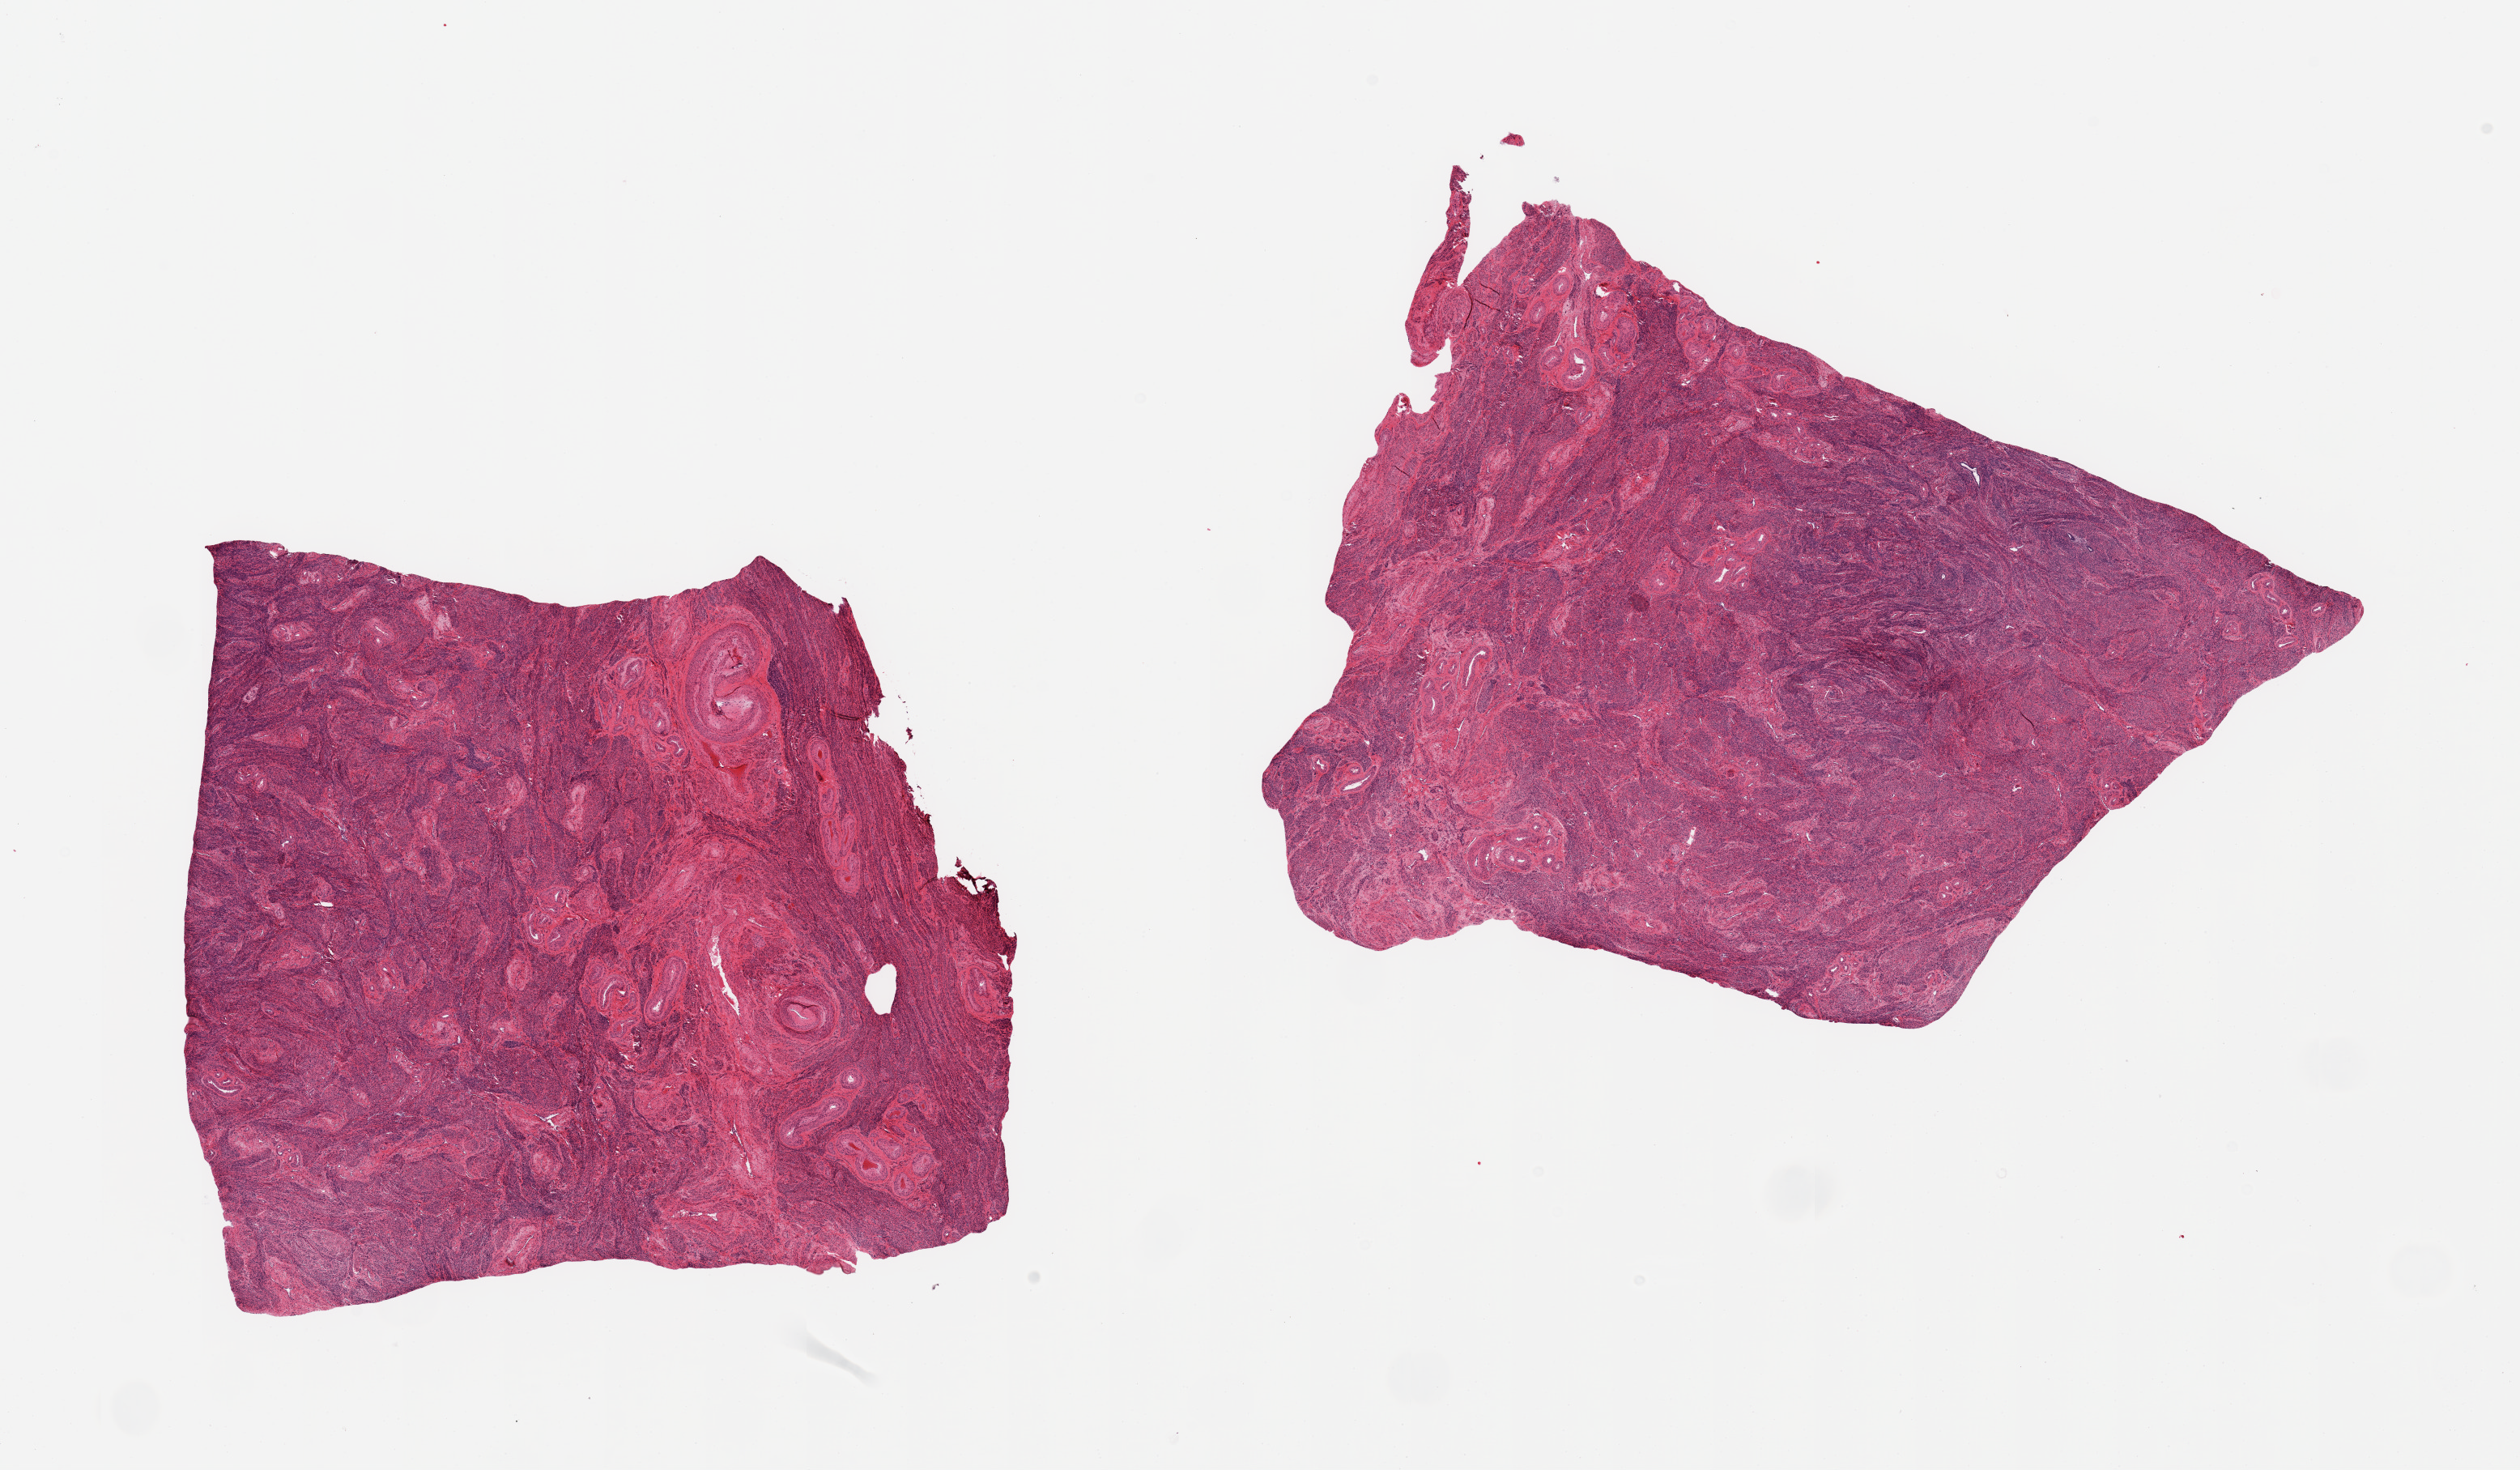
Digitized hematoxylin and eosin (H&E)-stained section, whole scanned area (about 24.6 x 14.4 mm, acquisition: 20x scan) shown as a low-resolution overview; PAXgene-fixed paraffin-embedded (PFPE) section; section of uterus (target tissue); tissue donor sample. Female donor.
- reviewer comment on this tissue sample: 2 pieces, all myometrium; no endometrial elements noted